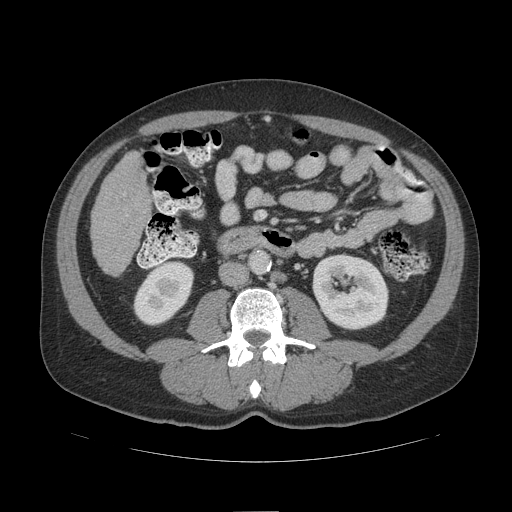
Contrast-enhanced abdominal CT (liver protocol), one axial slice. Slice 31 of 109 in the series (ordered by position). Reconstruction kernel STANDARD. Soft-tissue window (W 400 / L 40 HU). 2.5 mm slice thickness. 512 × 512 image matrix, field of view 420 × 420 mm. From the clinical record (not read from this slice): diagnosis: hepatocellular carcinoma (patient treated with transarterial chemoembolisation; whether this scan precedes or follows treatment is not stated here); TNM stage (as recorded): Stage-IIIB; Child-Pugh class: A; tumour differentiation: poorly differentiated; tumour nodularity: multinodular.
Structures marked on this image (semi-automatic segmentation, software-assisted and operator-edited):
- liver parenchyma outside the tumour (the mass and vessels are separate outlines, so this box may not span the whole liver): box from (x=92, y=151) to (x=150, y=274) px